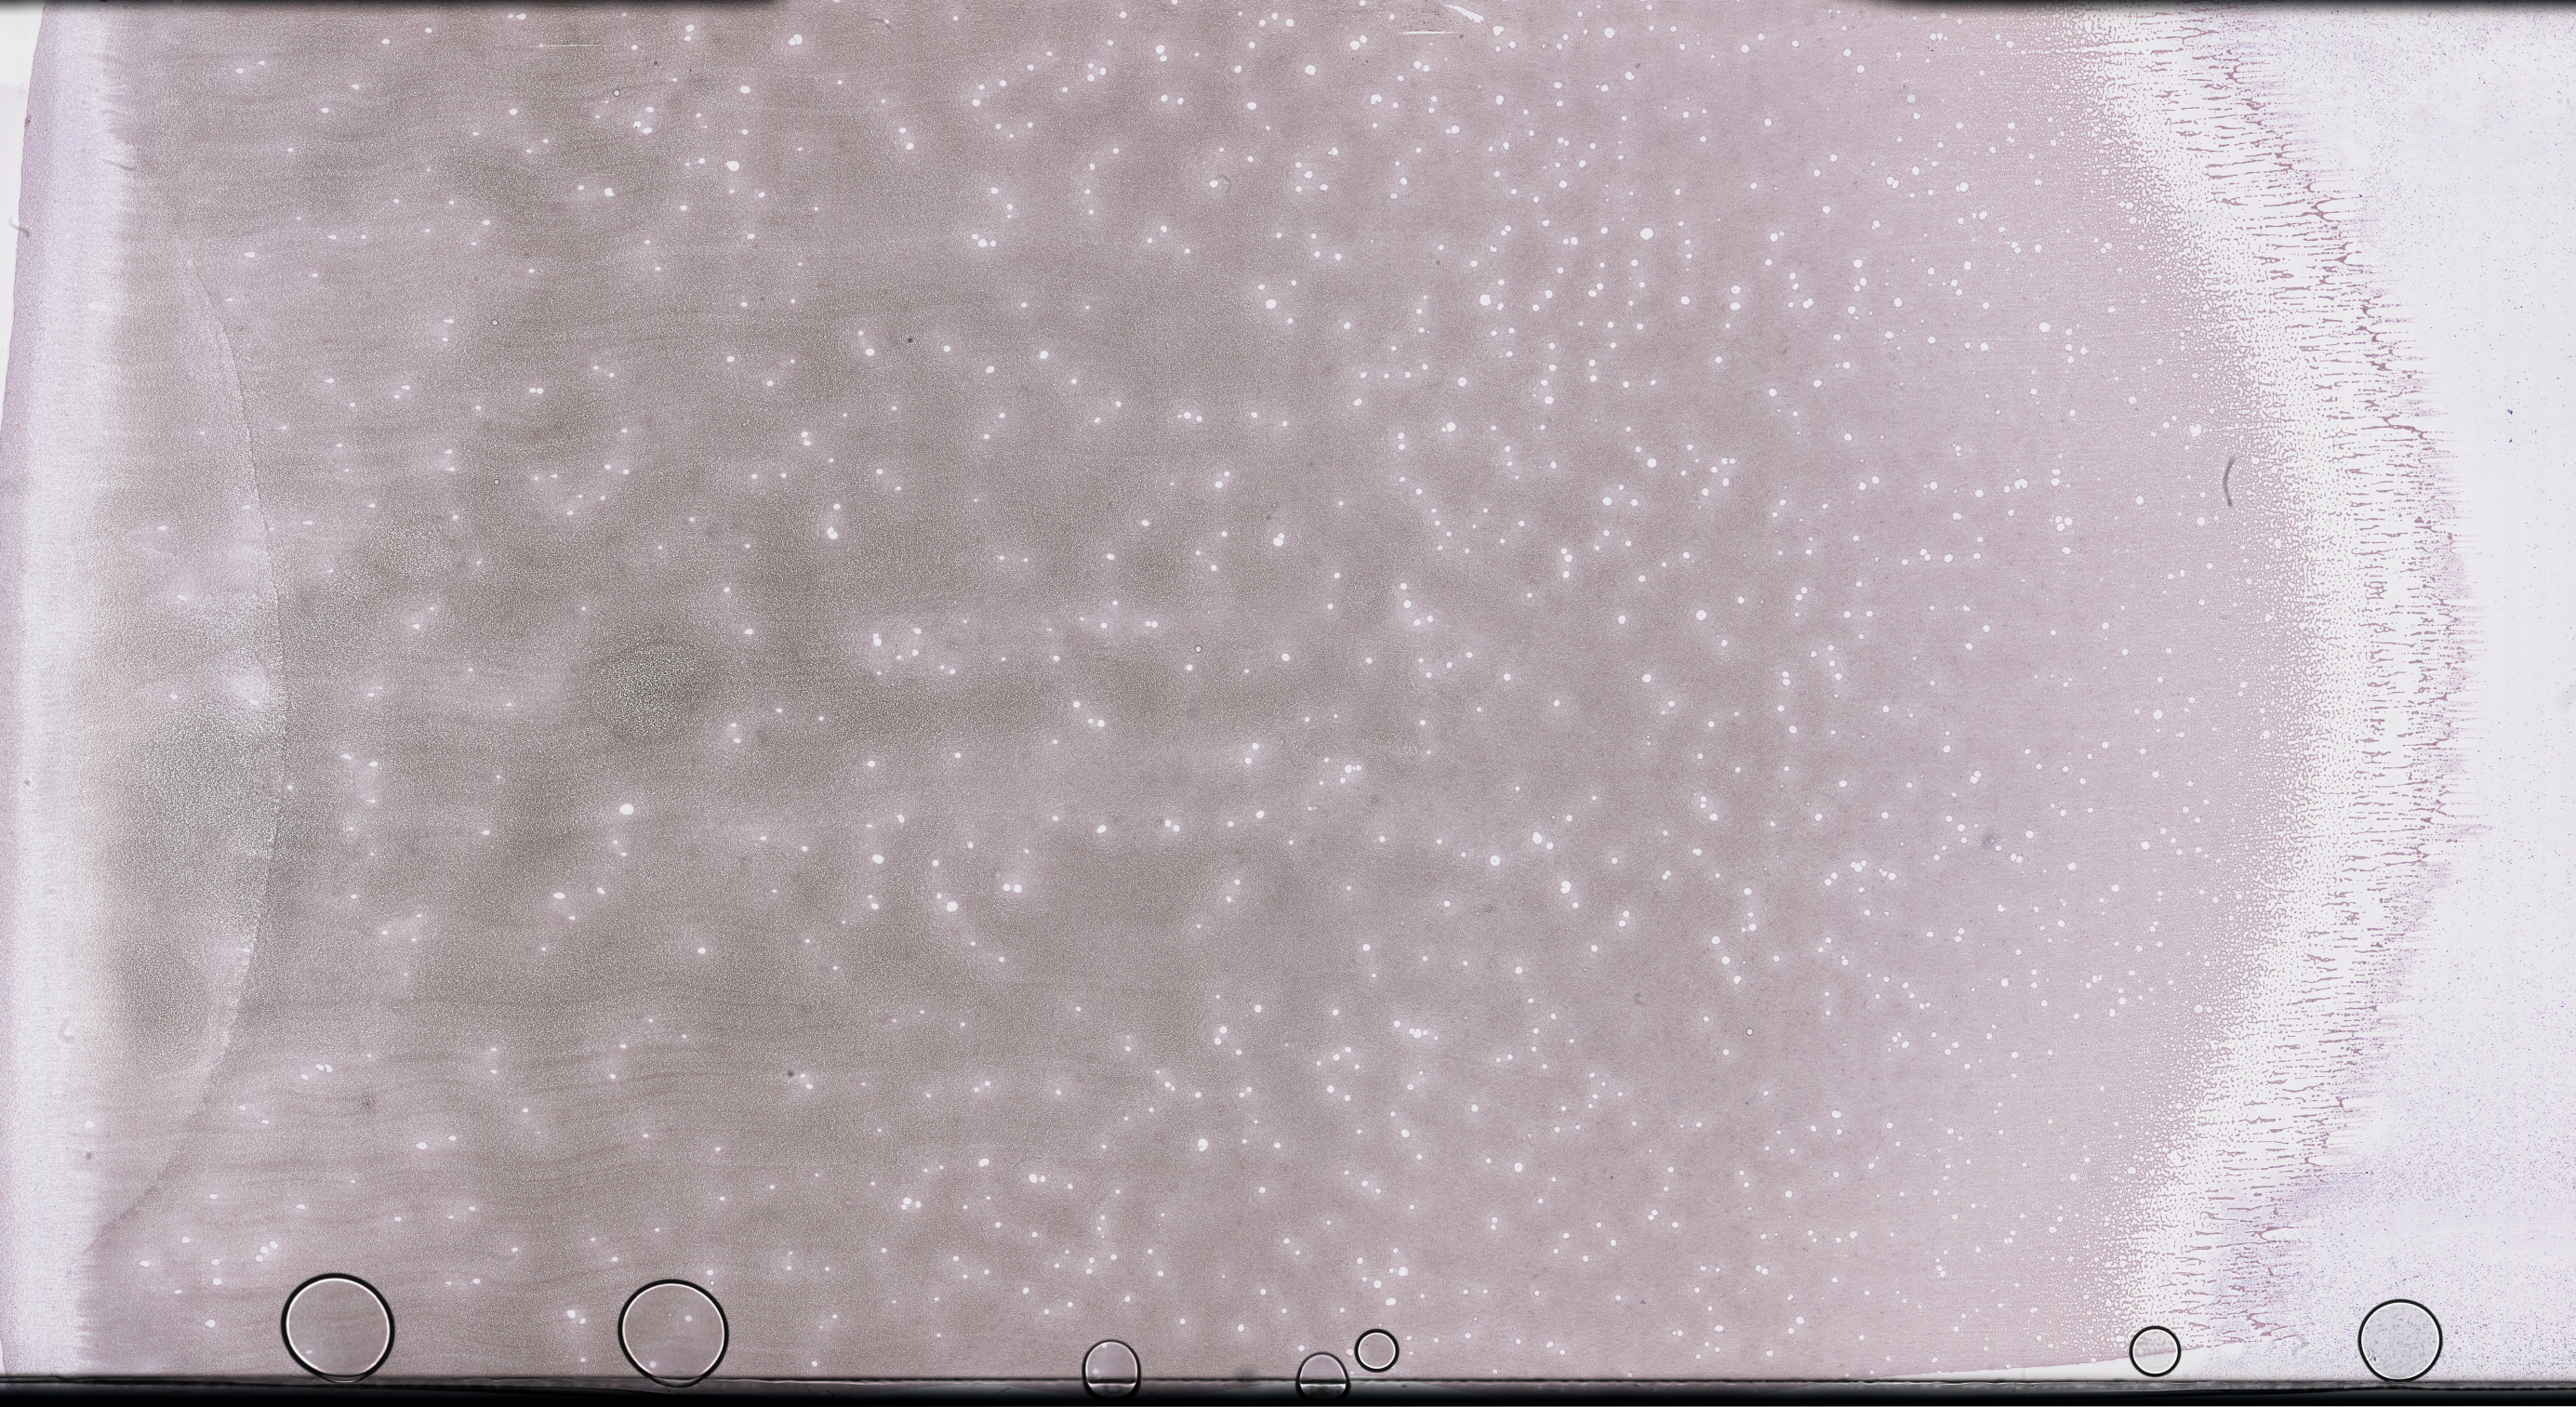
Wright–Giemsa-stained whole blood smear, whole-slide image, a low-resolution overview of the entire scanned area, about 44.7 x 24.4 mm; collected on treatment. Patient sex: female.
• patient diagnosis: Plasma Cell Myeloma